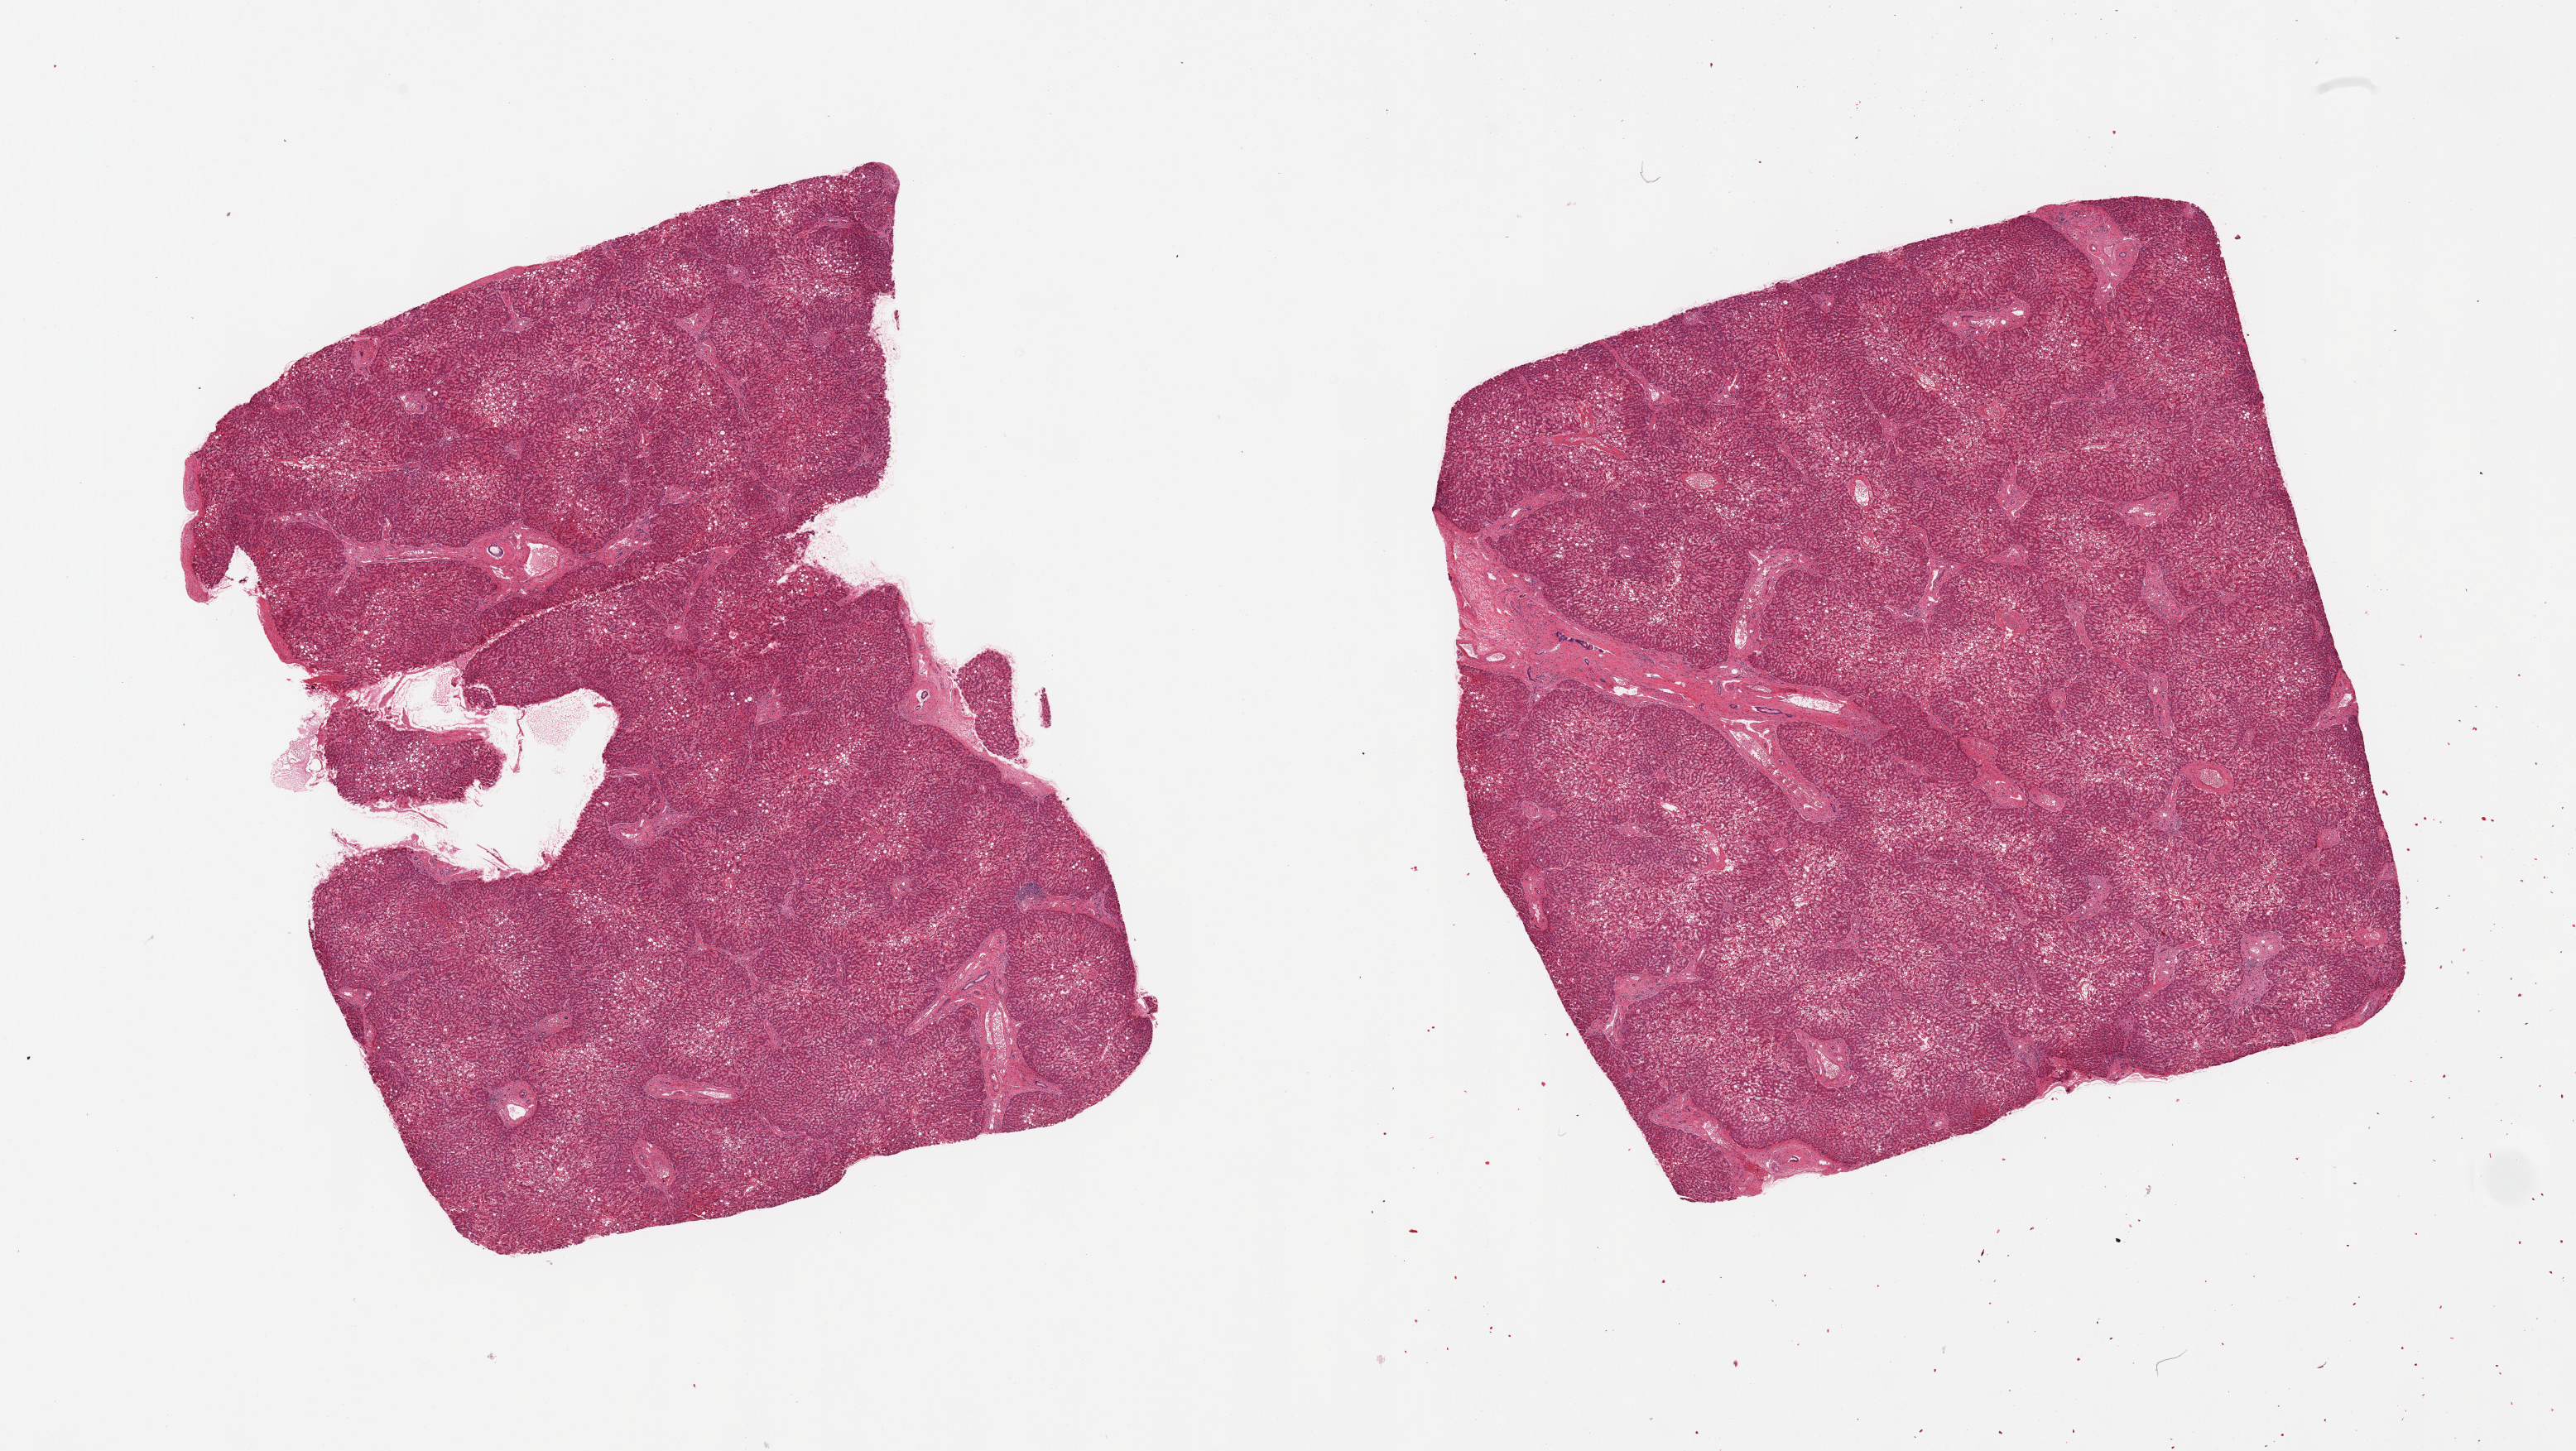
Whole-slide image, haematoxylin and eosin stain — shown as a low-resolution overview of the whole scanned area (about 24.6 x 13.9 mm, slide scanned at 20x). PAXgene-fixed paraffin-embedded (PFPE) section. Section of liver (target tissue). Tissue donor sample. Donor sex: male.
Pathologist's review note for this sample: 2 pieces; includes portion of capsule (target is 1 cm below capsule), mild steatosis, passive congestion, focal portal chronic inflammation.